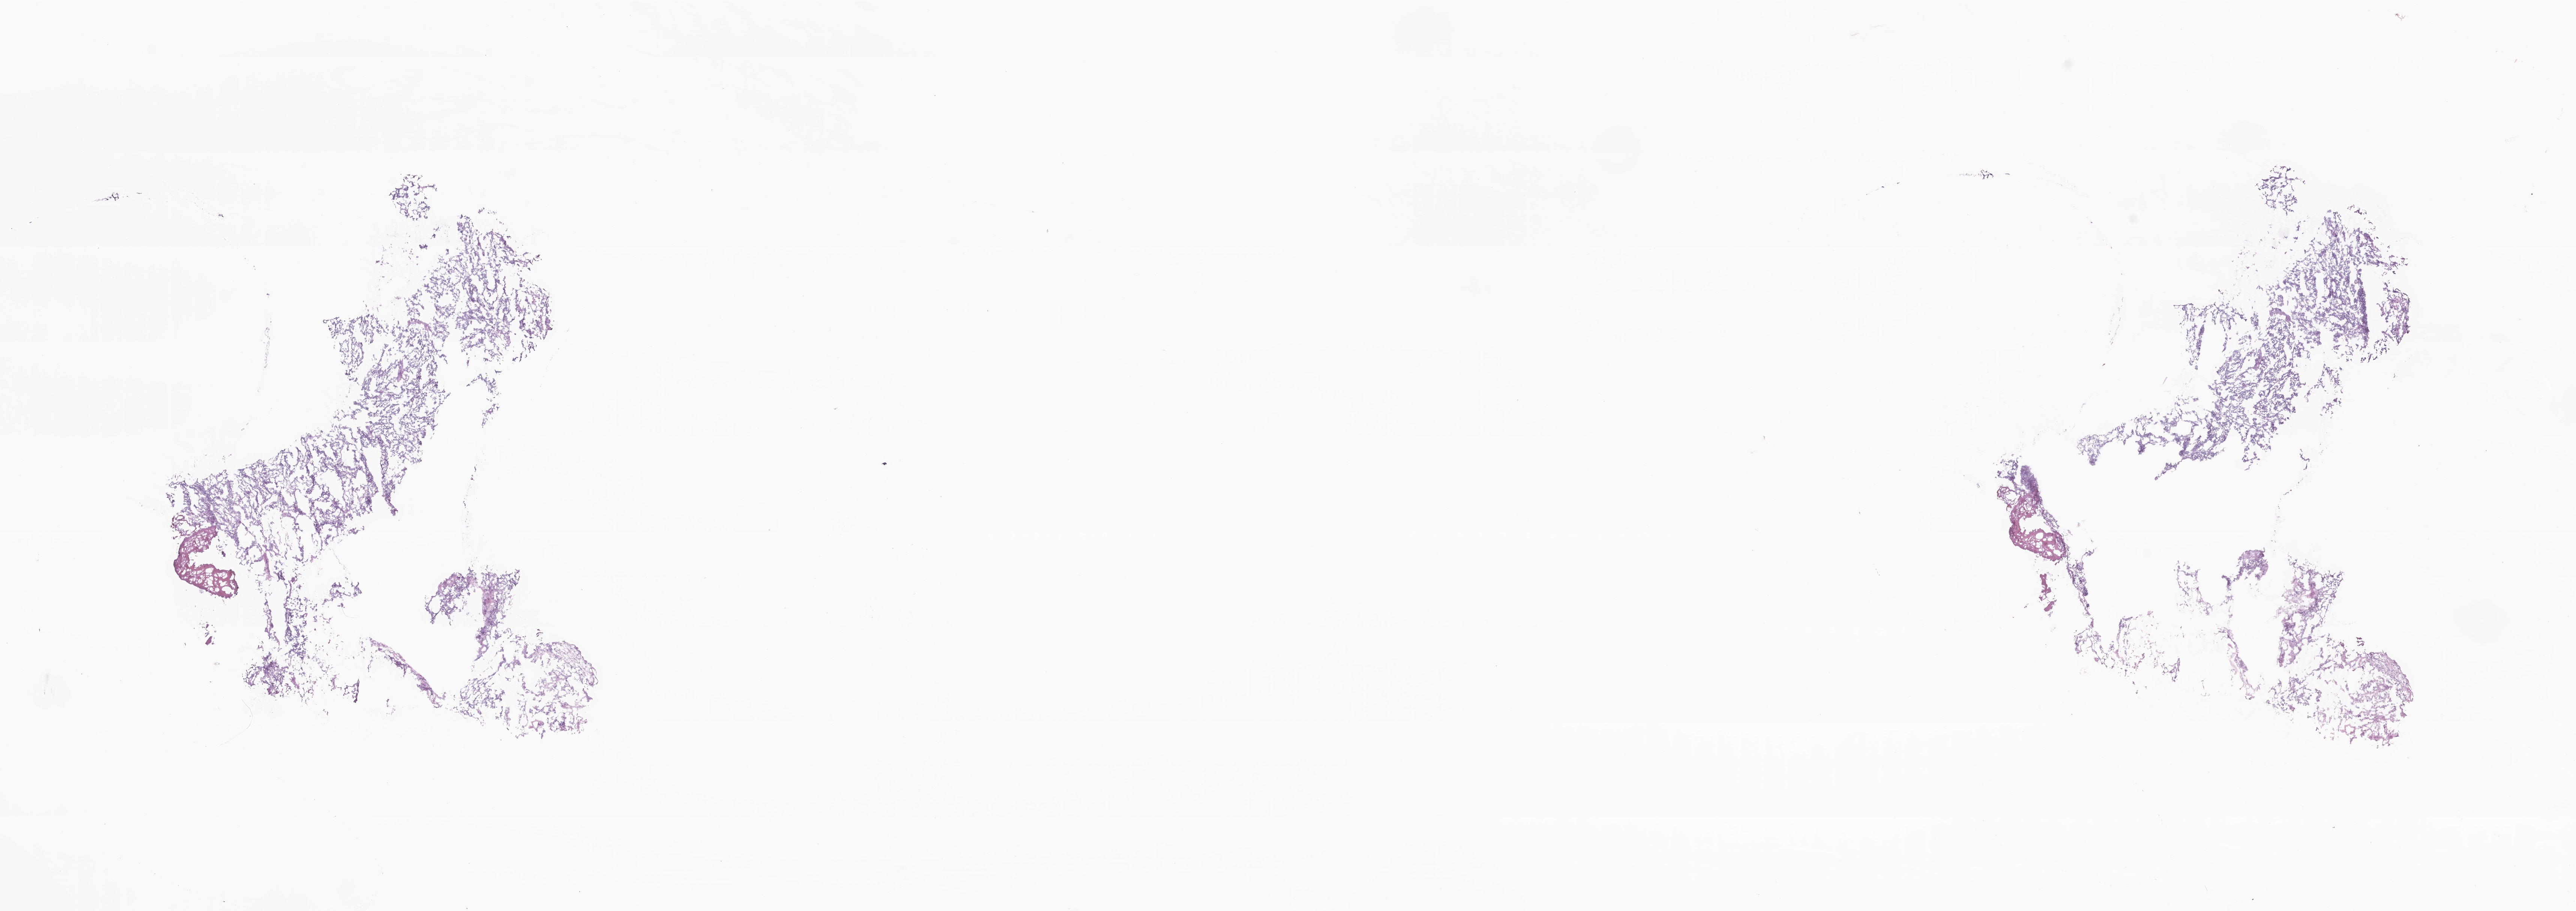
Whole-slide image, haematoxylin and eosin stain — shown as a low-resolution overview of the whole scanned area (about 29.0 x 10.2 mm). Cryosection. Primary tumor. Anatomic site: kidney. Male patient; age at initial diagnosis 50 years. Tumor grade: G3 (poorly differentiated). Slide review estimates, as recorded: tumor cells 67%, tumor nuclei 86%, stromal cells 22%, necrosis 0%, normal cells 11%. Inflammatory infiltration, as recorded: lymphocyte infiltration 0%, monocyte infiltration 0%, neutrophil infiltration 0%.
- AJCC pathologic stage: Stage III
- diagnosis: Clear cell adenocarcinoma, NOS